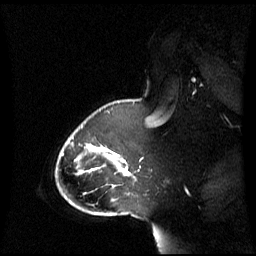
Breast MRI (dynamic contrast-enhanced), one sagittal slice; slice 47 of 60 in the series (ordered by position); dynamic contrast-enhanced series, image 2 of 3 at this slice position (ordered by acquisition); 1.5 T; TE 4.2 ms, TR 8.4 ms; 2.8 mm slice thickness; 256 × 256 image matrix, field of view 270 × 270 mm. Female patient, age 43 years. From the clinical record (not read from this slice): setting: breast cancer imaged before/during neoadjuvant chemotherapy; receptor status: triple-negative.
Outlined on this slice (semi-automatic segmentation, software-assisted and operator-edited):
- analysis volume of interest (the breast-tissue region the enhancement analysis was run in; not a lesion): bounding box <65,118,142,198> (left, top, right, bottom; pixels)
- tumour enhancement mask (voxels above the 70 % enhancement threshold inside the analysis volume of interest): <98,146,128,168>